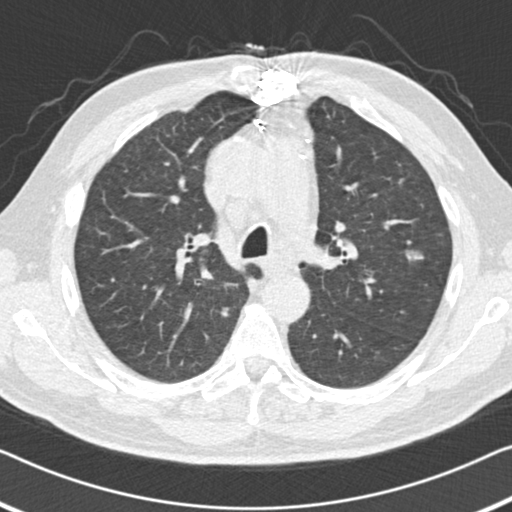
Low-dose screening chest CT, axial slice, baseline annual screen, lung window (W 1500 / L -600 HU), 2 mm slice thickness, standard (soft-tissue) reconstruction kernel (B30f), 120 kVp, slice 51 of 155 in the series, 512 × 512 image matrix. Male, age 64 years at enrolment. Current smoker at enrolment.
- Lesion marked by an expert reader, bounding box <387,228,443,279> (left, top, right, bottom; pixels).
- The screening reader recorded 2 non-calcified nodules or masses ≥4 mm on this exam; which of them this box marks is not recorded.
- Official screen result: positive, change unspecified: nodule(s) >= 4 mm or enlarging nodule(s), mass(es), or other non-specific abnormalities suspicious for lung cancer.
- Participant outcome: lung cancer diagnosed 133 days after this screen — adenocarcinoma, NOS, left upper lobe, poorly differentiated (G3), stage IA (AJCC 6th edition), 15 mm at pathology.